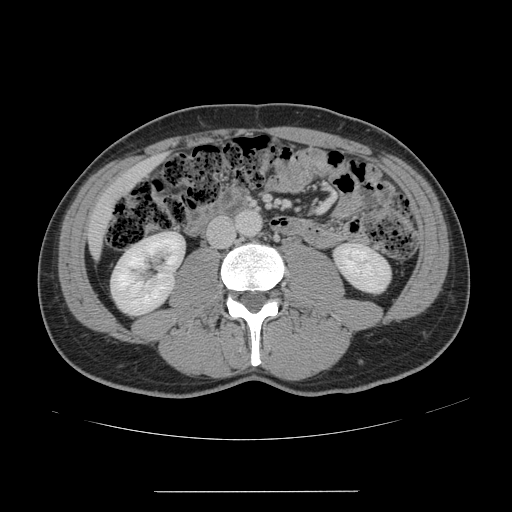
Contrast-enhanced abdominal CT, one axial slice. Slice 33 of 178 in the series (ordered by position). 120 kVp. Intravenous contrast given. Soft-tissue window (W 400 / L 40 HU). 2.5 mm slice thickness. 512 × 512 image matrix, field of view 401 × 401 mm. Male patient, age 53 years. From the clinical record (not read from this slice): diagnosis: colorectal cancer liver metastases, imaged before liver resection; multiple liver metastases: yes; largest metastasis: 2.4 cm; chemotherapy before resection: yes.
Outlined on this slice (expert manual segmentation):
- liver: bounding box (x1, y1, x2, y2) in pixels: (90, 158, 160, 254)